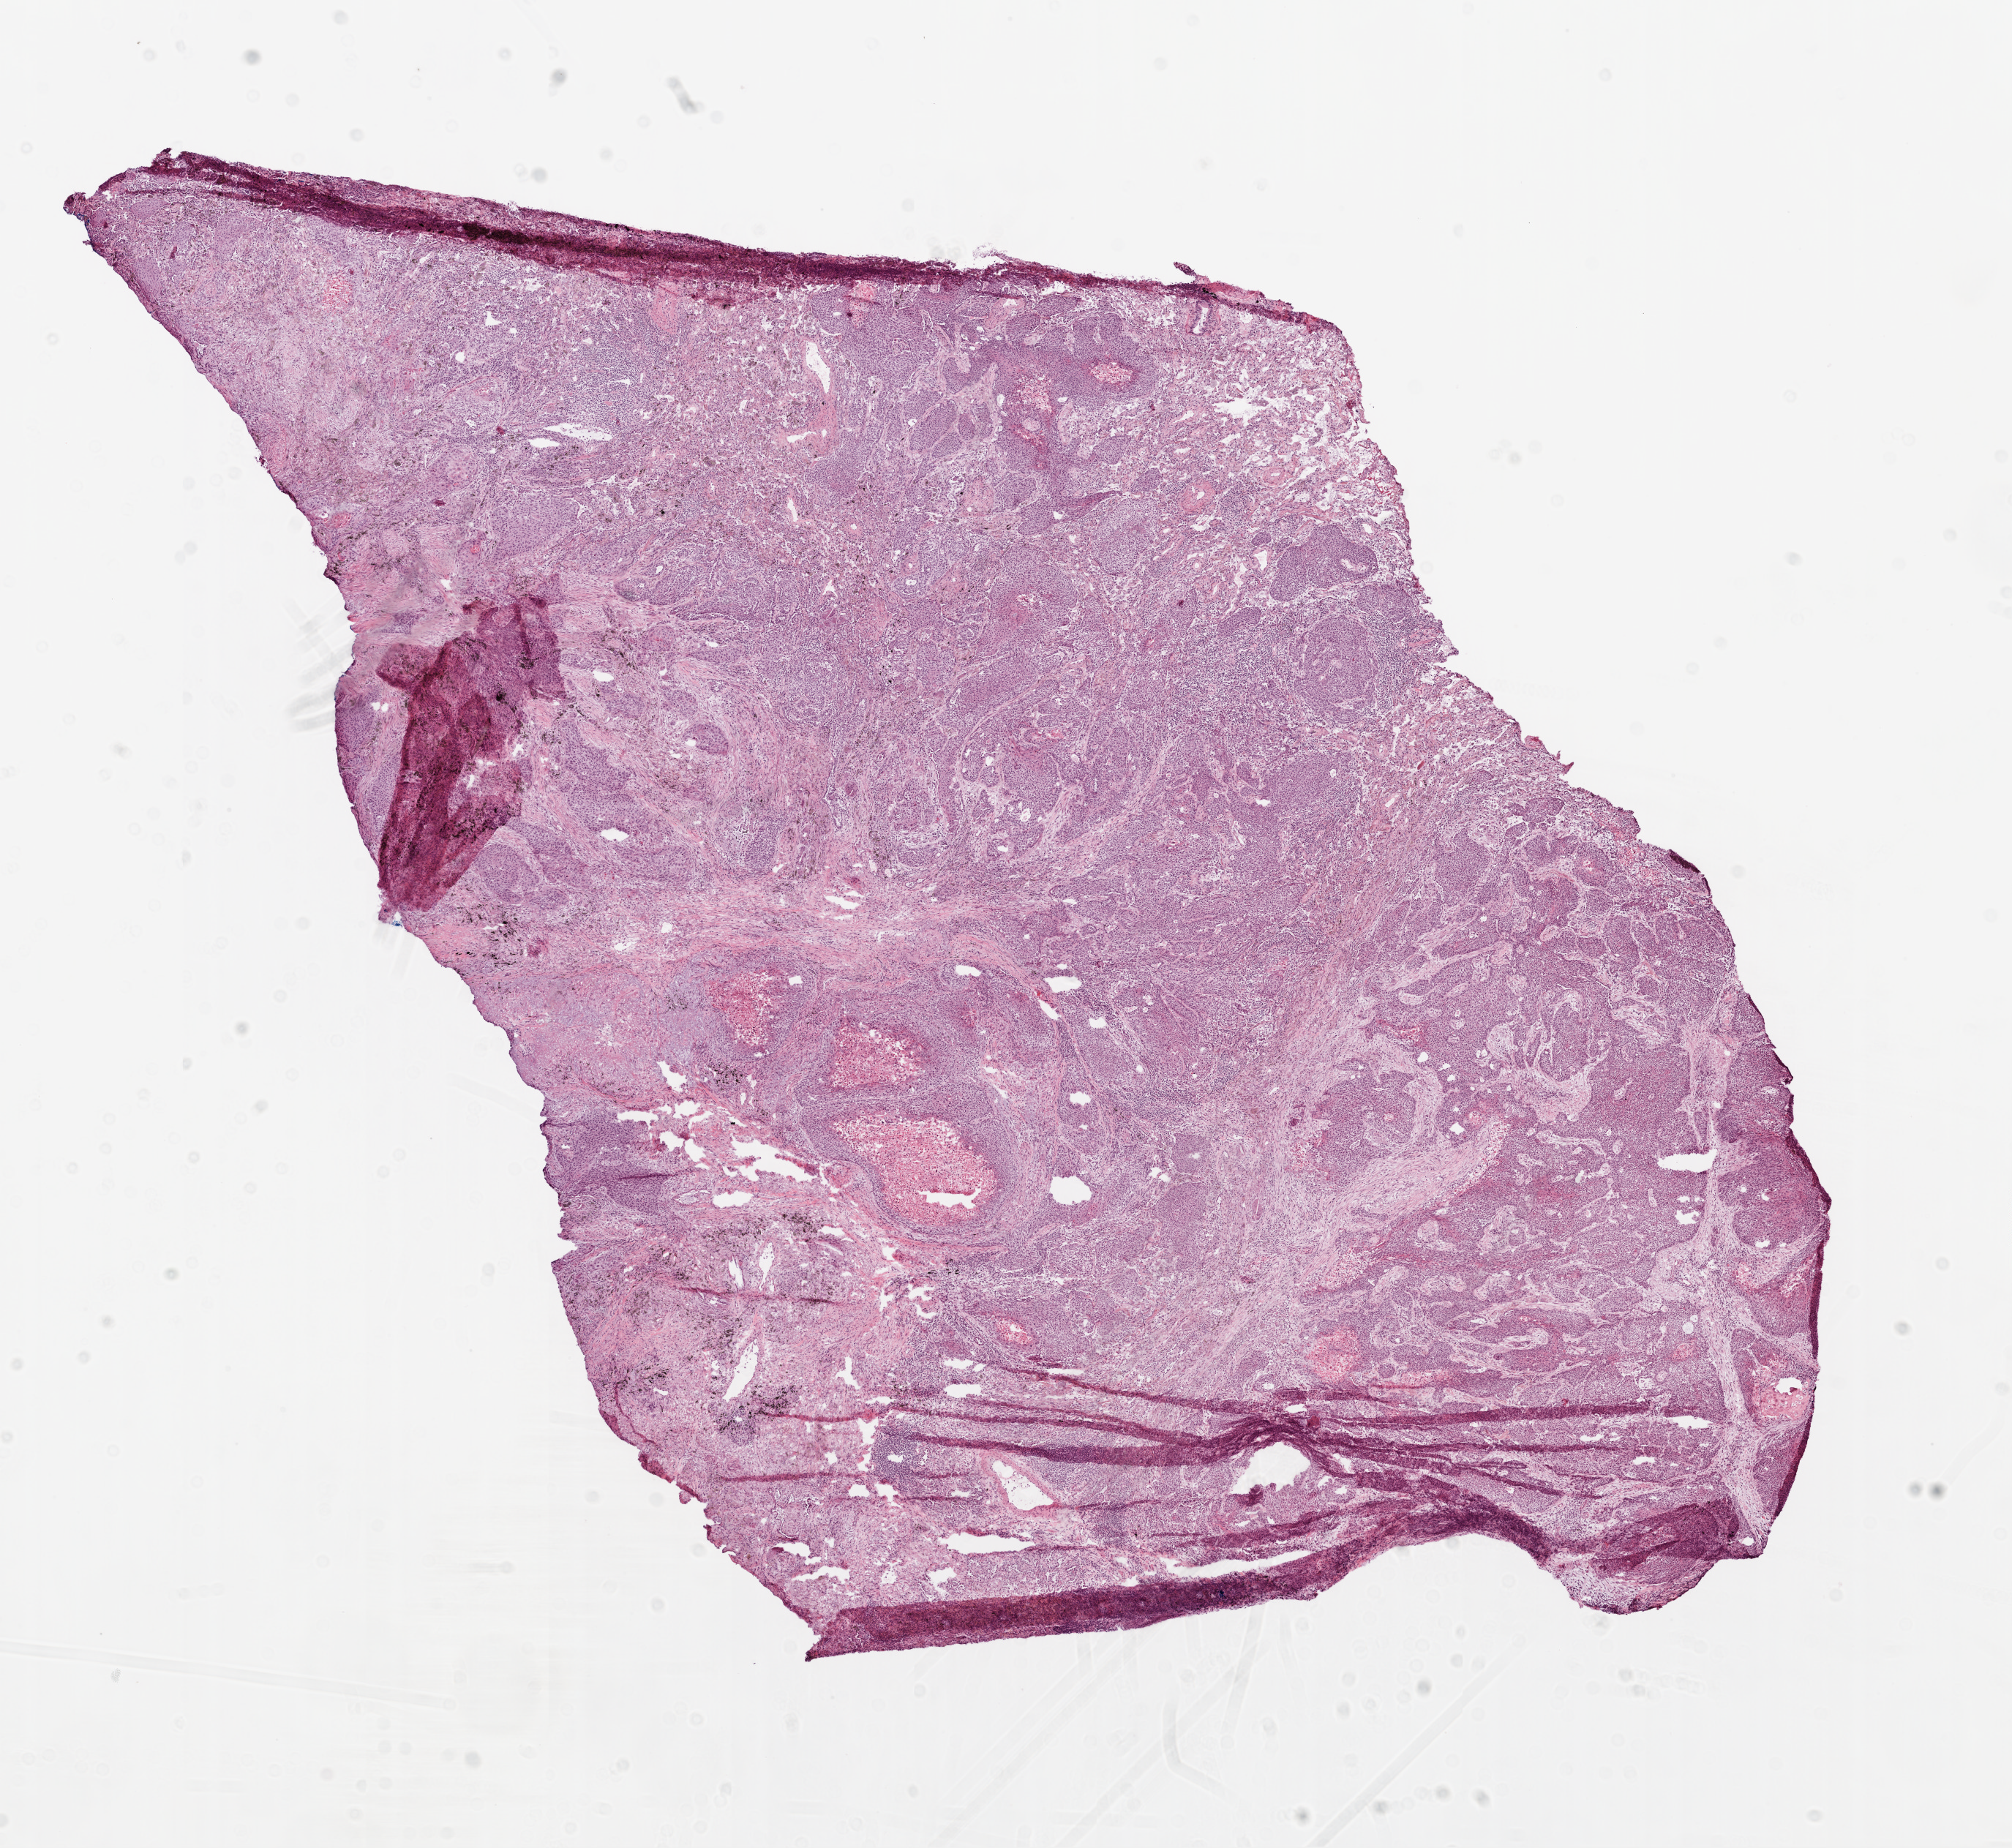
H&E whole-slide image, a low-resolution overview of the entire scanned area, about 11.0 x 10.1 mm (acquisition: 20x scan); frozen section from the top of the tissue portion; primary tumour sample from the lung. Patient: female, age at initial diagnosis 67 years. Composition of this section per pathologist review: tumour cells 82%, tumour nuclei 85%, normal cells 3%, stromal cells 10%, necrosis 5%.
AJCC pathologic stage: IIA. Diagnosis: Squamous cell carcinoma, NOS (upper lobe, lung).